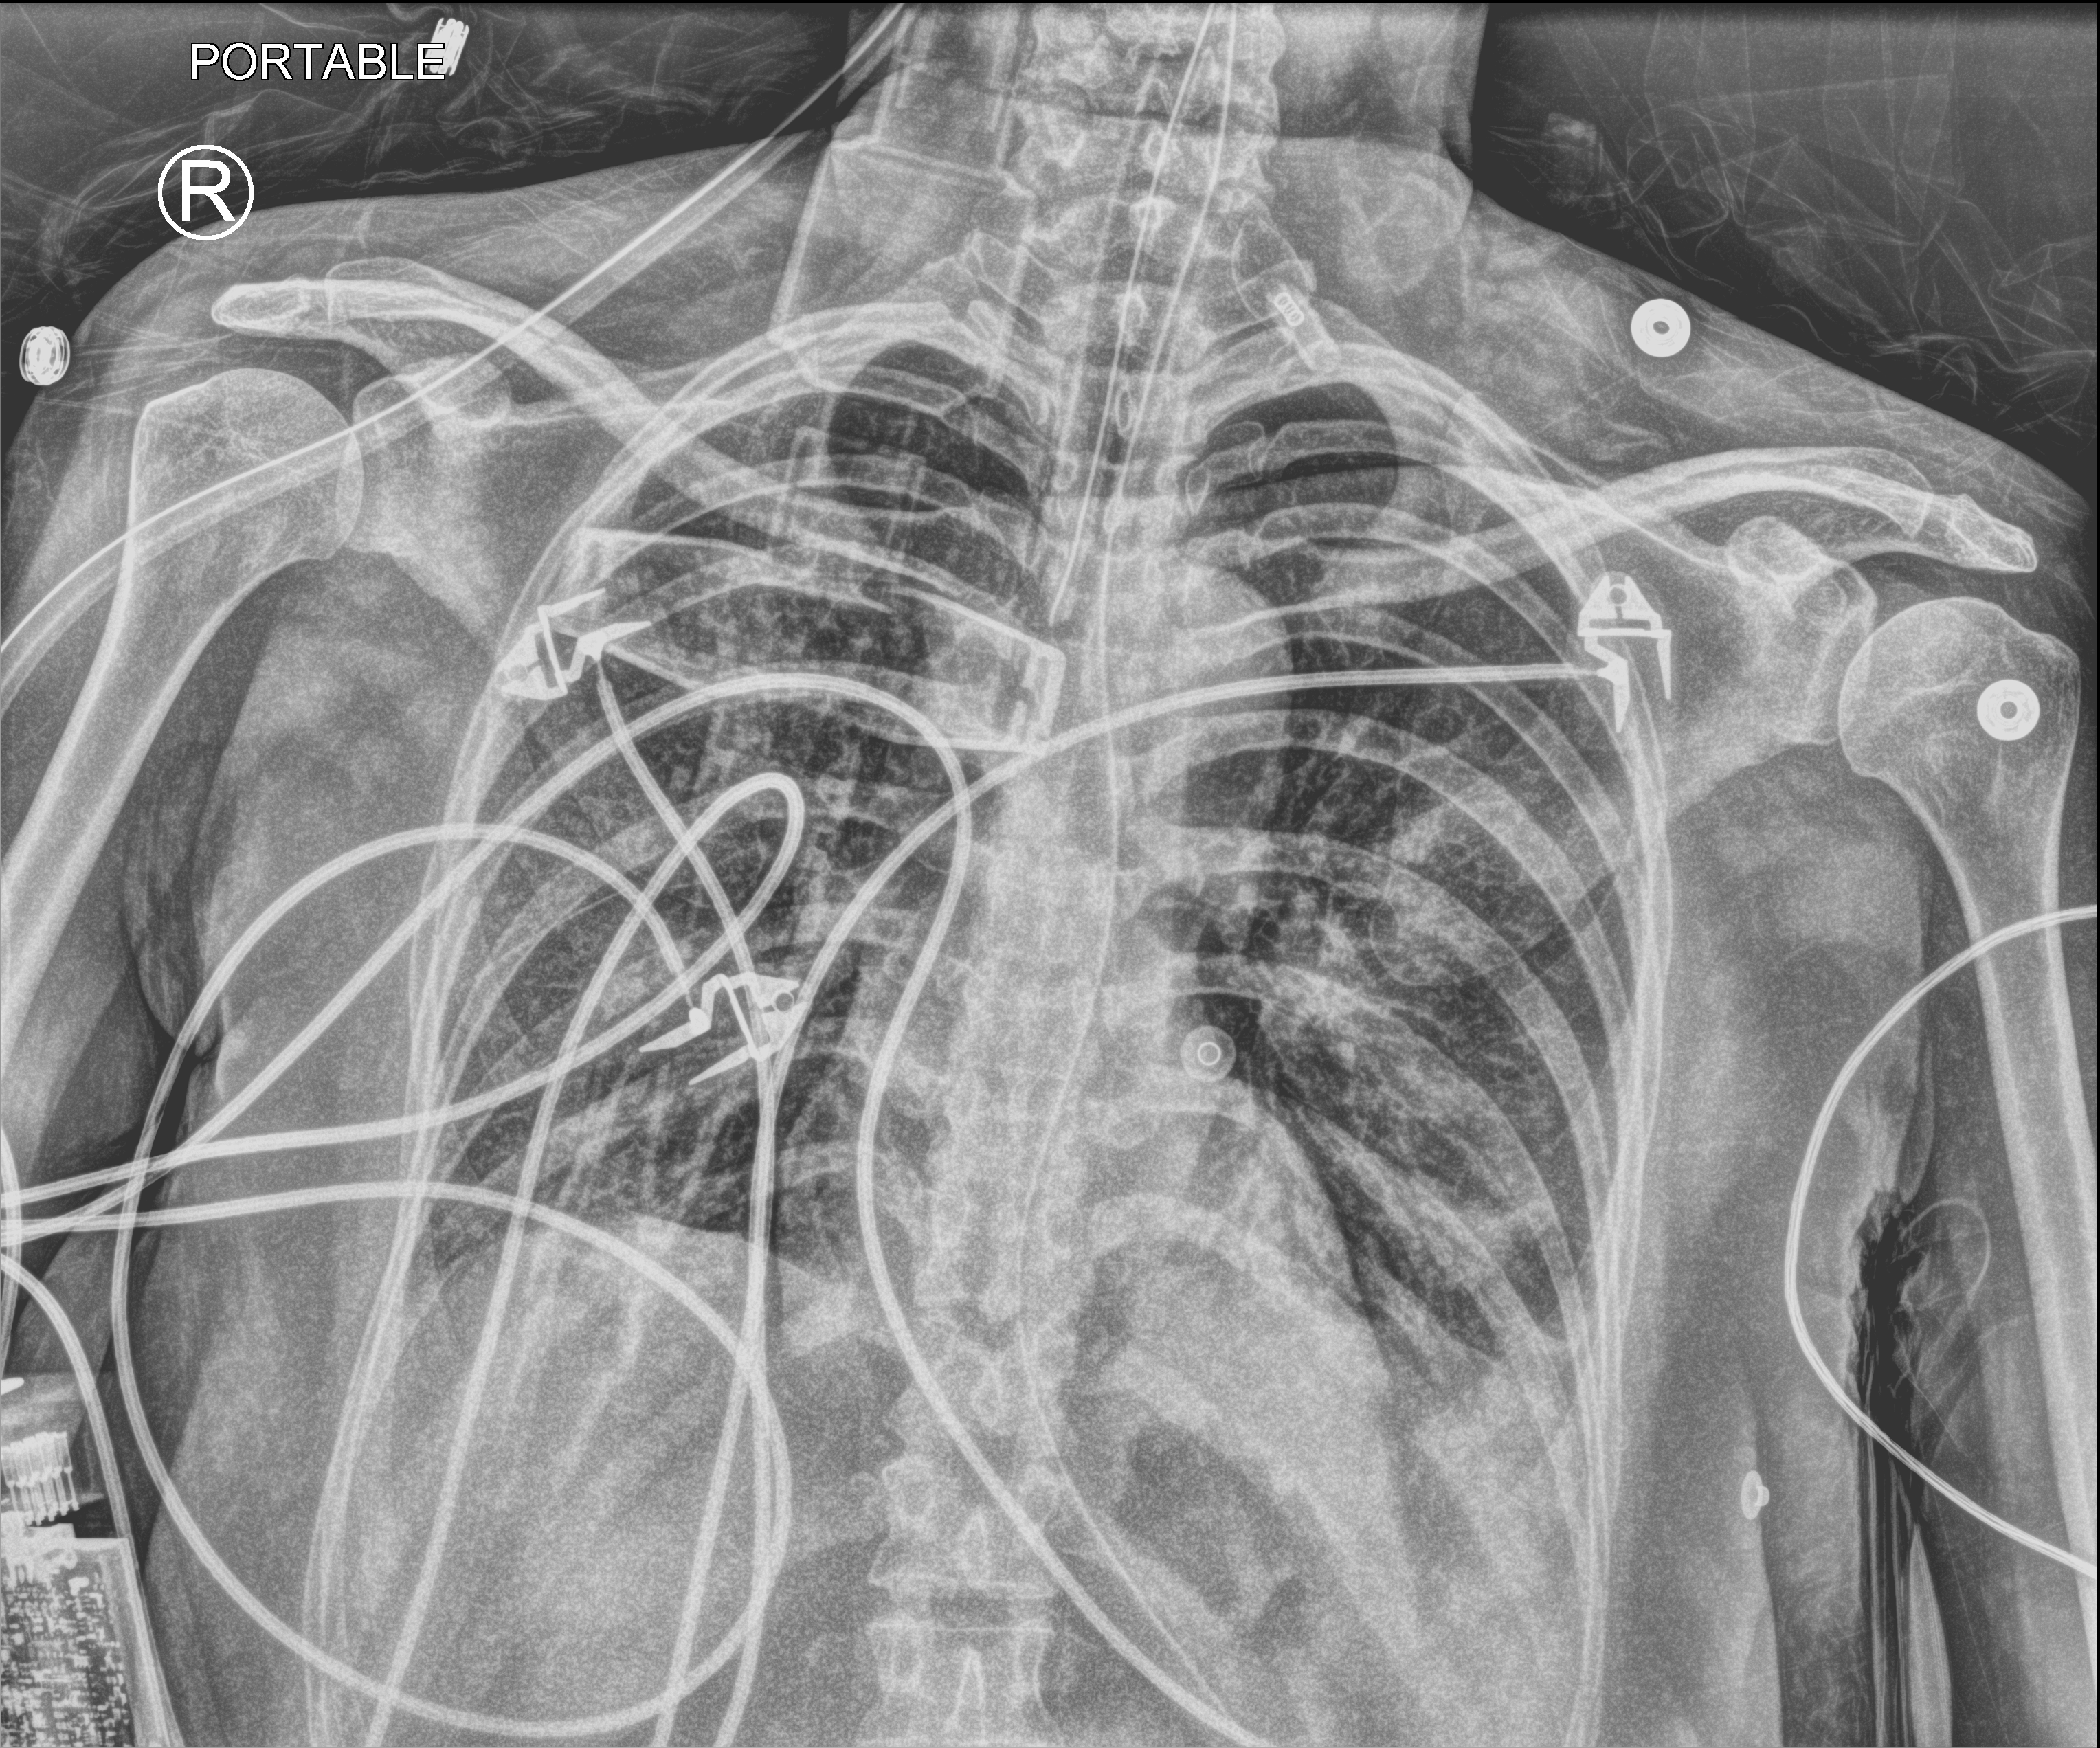
Bedside chest radiograph (computed radiography), anteroposterior (AP) projection. Female patient hospitalised with COVID-19, age 18–59 years.
Admission-level facts for this patient (not findings on this image; timing relative to this image not recorded):
- admitted to intensive care during this hospital stay: yes
- mechanically ventilated during this hospital stay: yes